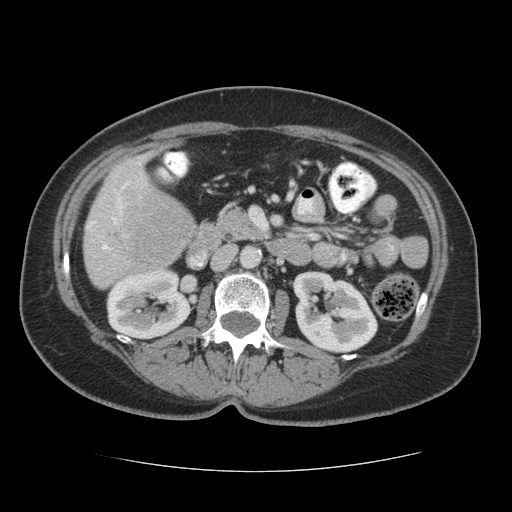
Contrast-enhanced abdominal CT (liver protocol), one axial slice. Position 16 of 75 along the scan axis. Reconstruction kernel STANDARD. 140 kVp. Soft-tissue window (W 400 / L 40 HU). 2.5 mm slice thickness. 512 × 512 image matrix, field of view 360 × 360 mm. From the clinical record (not read from this slice): diagnosis: hepatocellular carcinoma (patient treated with transarterial chemoembolisation; whether this scan precedes or follows treatment is not stated here); TNM stage (as recorded): Stage-I; Child-Pugh class: A; tumour differentiation: moderately differentiated; tumour nodularity: uninodular.
Annotated regions visible in this slice (semi-automatically segmented with operator editing):
- liver parenchyma outside the tumour (the mass and vessels are separate outlines, so this box may not span the whole liver): bounding box [x1, y1, x2, y2] px = [84, 150, 192, 288]
- mass: [114, 174, 198, 272]
- liver vessels: [87, 162, 141, 250]